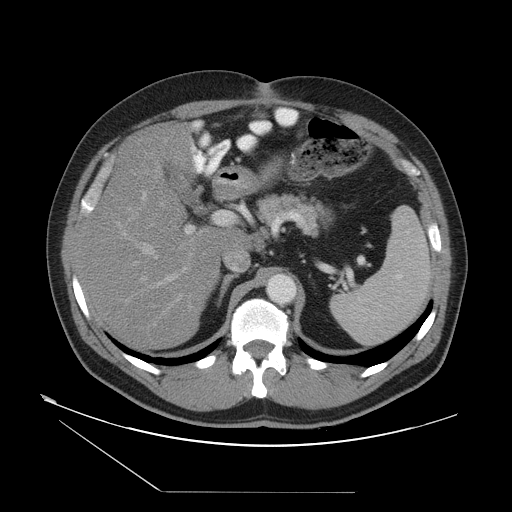
Contrast-enhanced abdominal CT, one axial slice. Position 30 of 55 along the scan axis. Intravenous contrast given. Soft-tissue window (W 400 / L 40 HU). 5 mm slice thickness. 512 × 512 image matrix, field of view 454 × 454 mm. Male patient, age 59 years. Case-level facts recorded for this patient, not image findings: diagnosis: colorectal cancer liver metastases, imaged before liver resection; multiple liver metastases: yes; largest metastasis: 0.3 cm.
Structures marked on this image (manually delineated by an expert):
- hepatic veins: bounding box <133,148,194,326> (left, top, right, bottom; pixels)
- liver: <83,122,244,350>
- planned liver remnant (the part of the liver to remain after resection): <83,136,244,350>
- portal vein (with intrahepatic branches): <156,141,236,313>